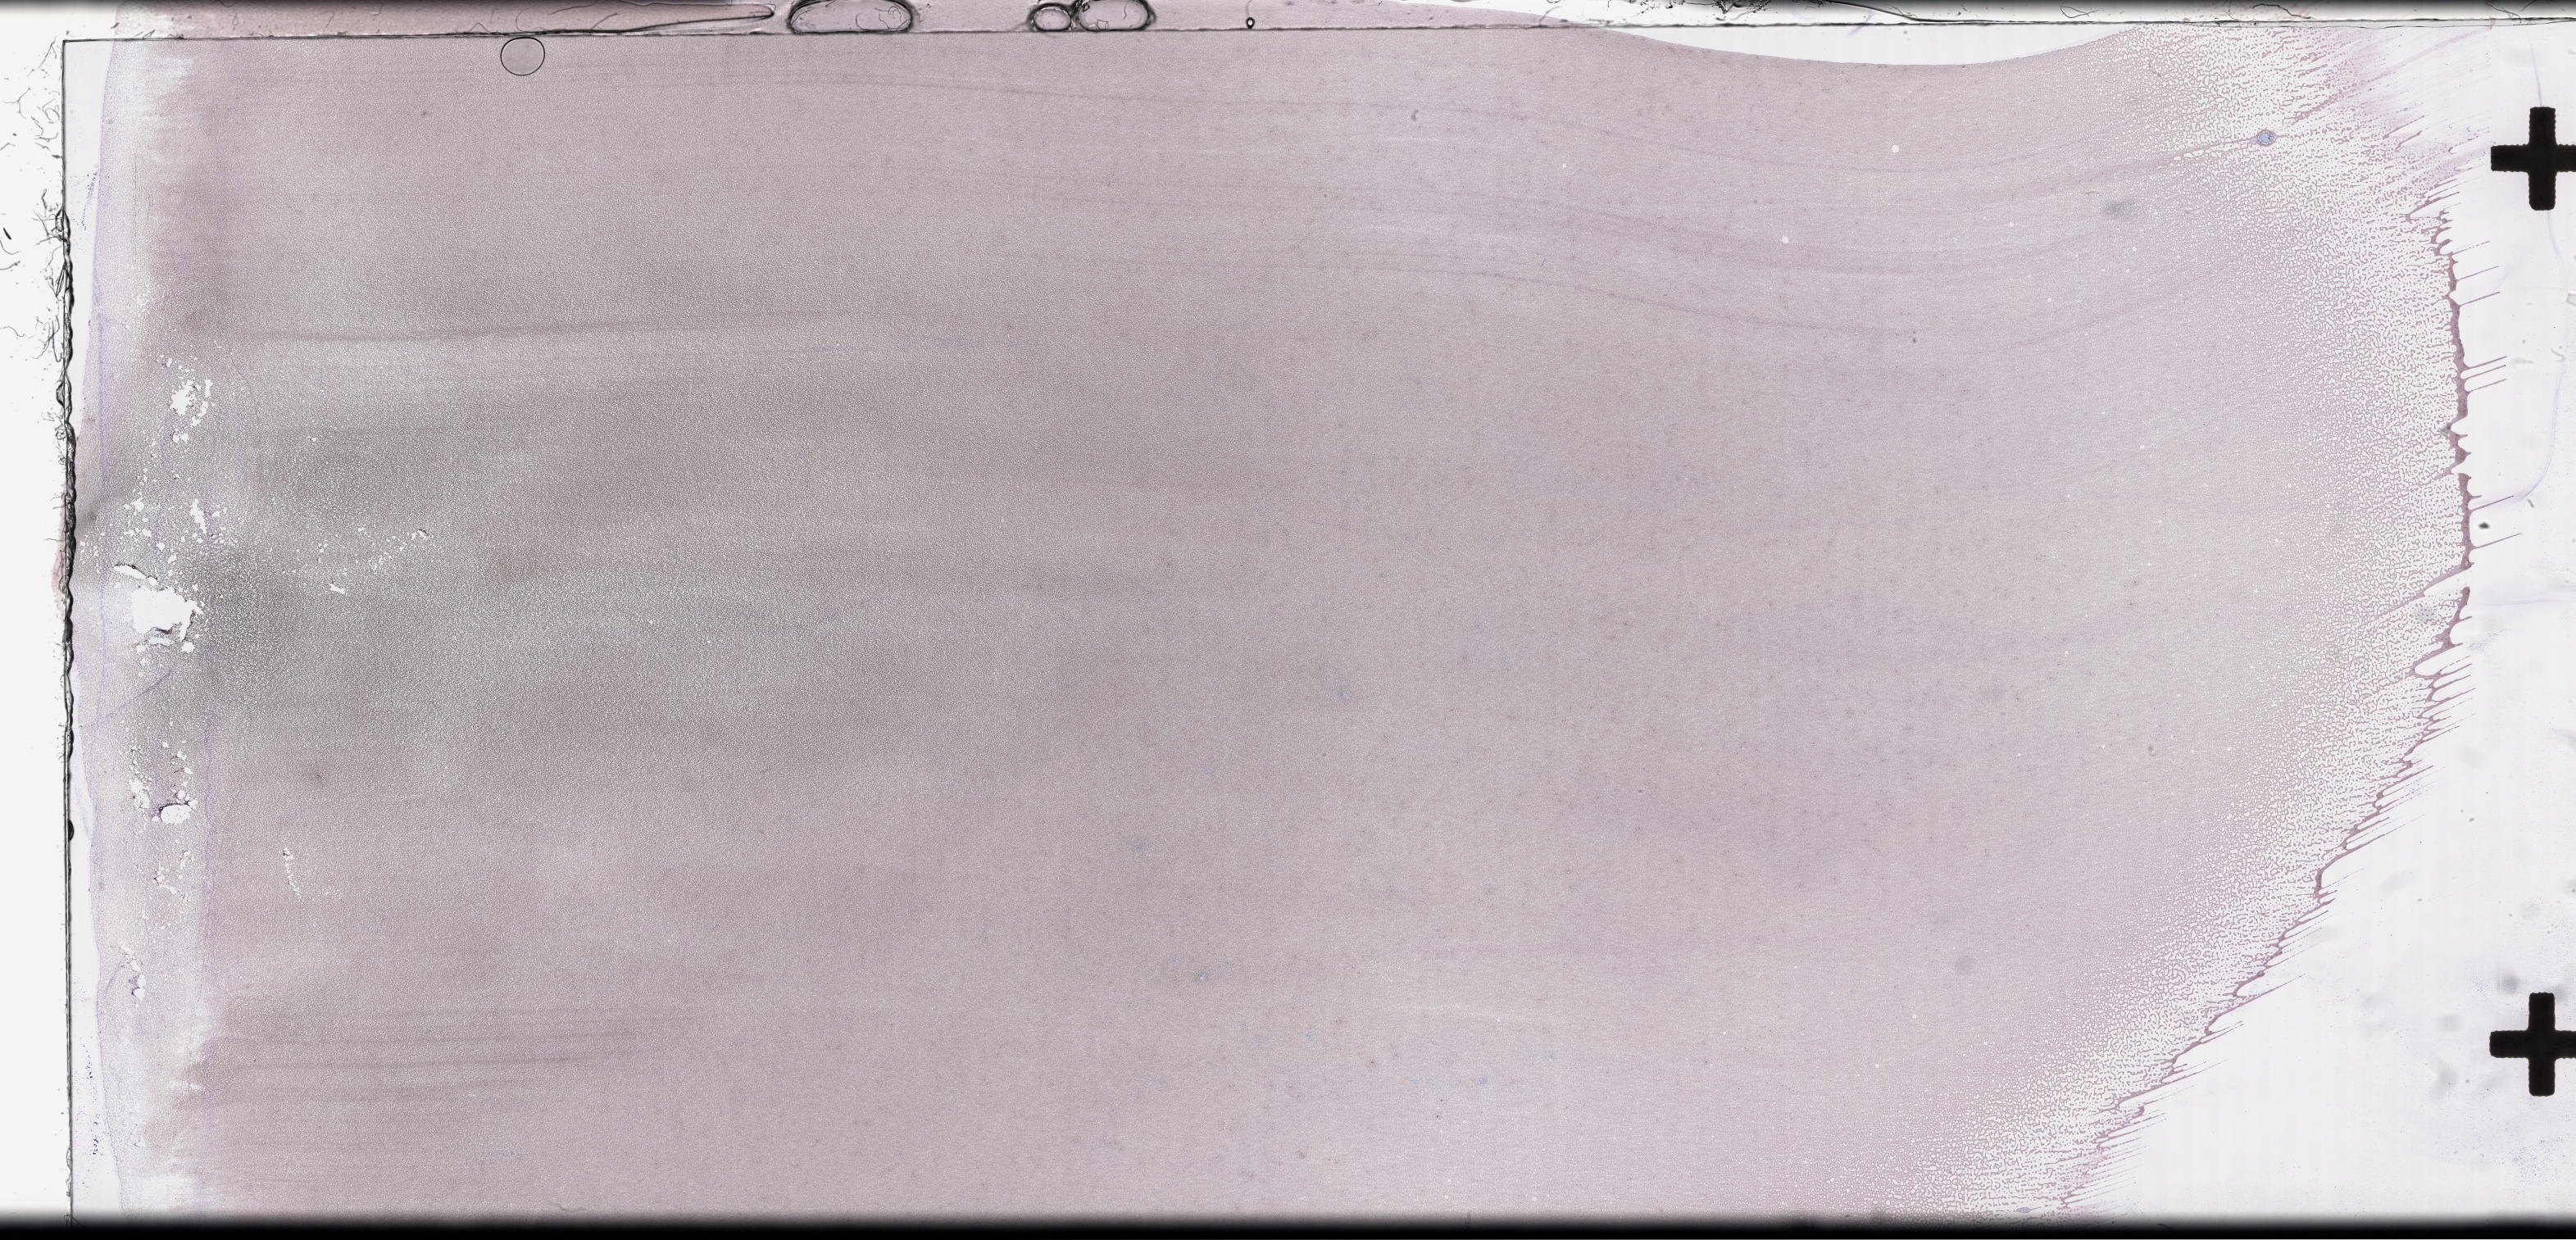
Whole-slide image of a whole blood smear, Wright-Giemsa stain — a low-resolution overview of the entire scanned area, about 50.8 x 24.4 mm, smear from an EDTA sample. Patient sex: male.
Patient diagnosis: Plasma Cell Myeloma.